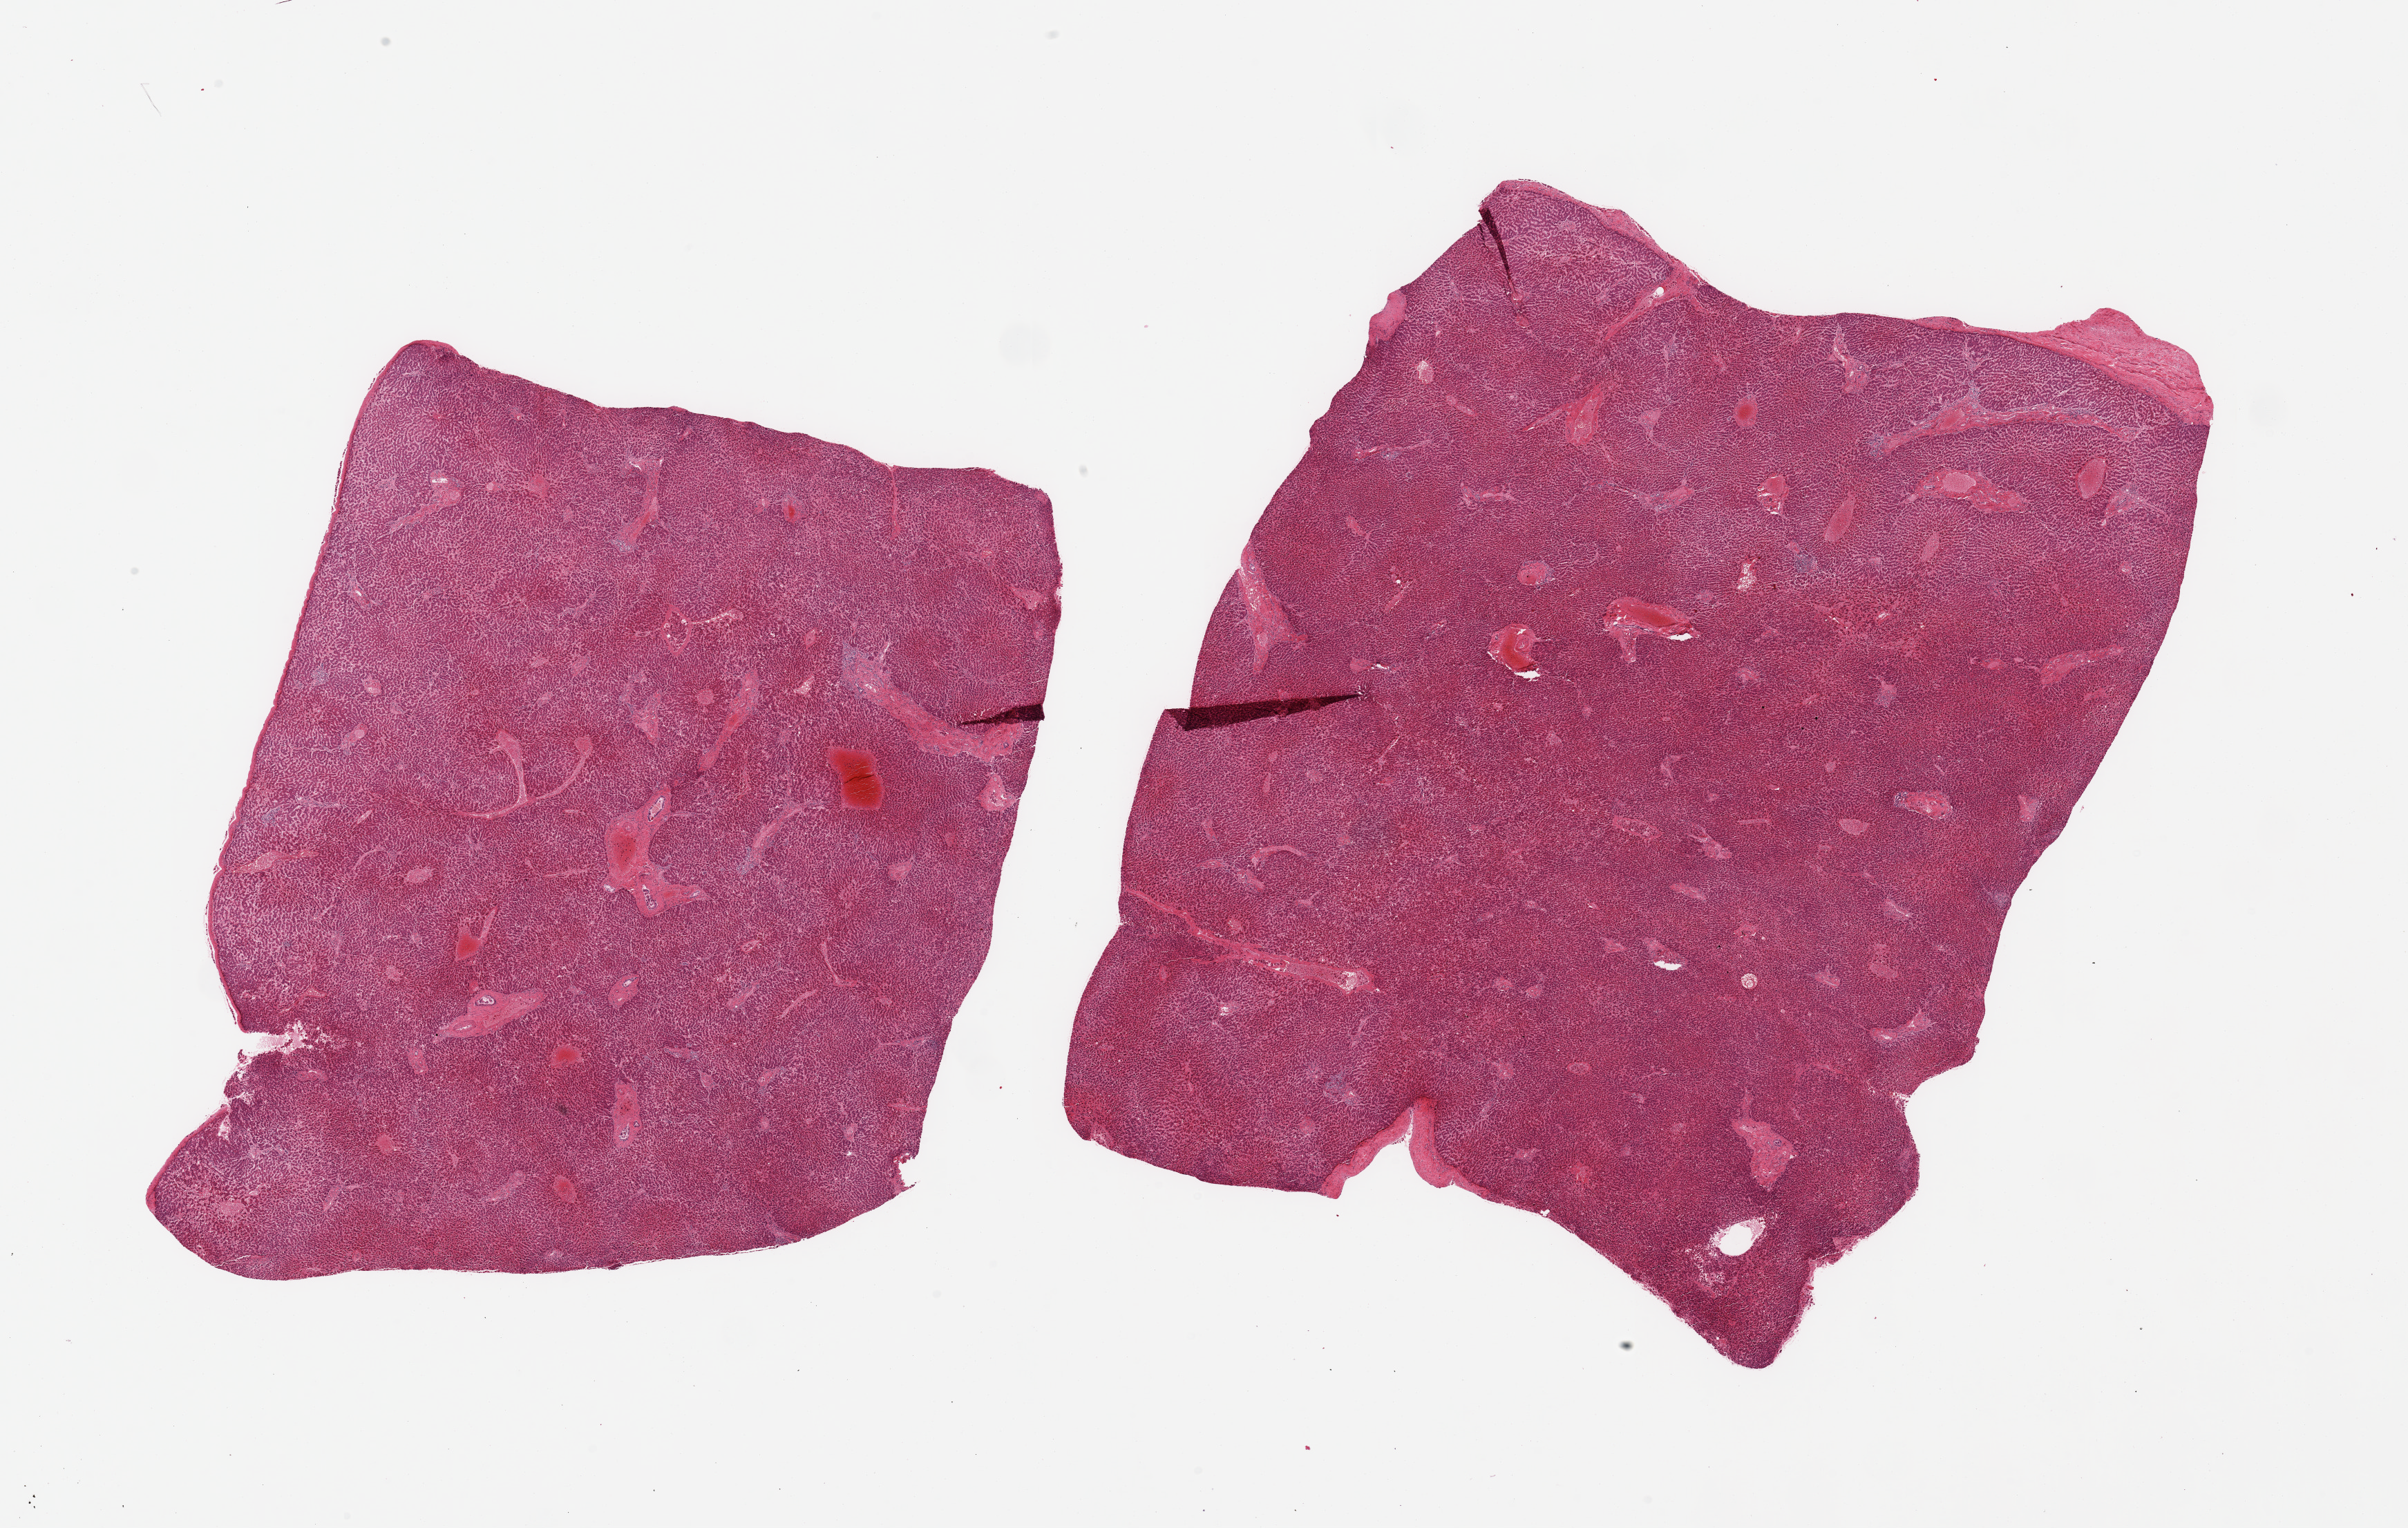
H&E whole-slide image, whole scanned area (about 27.6 x 17.5 mm, acquisition: 20x scan) shown as a low-resolution overview, PAXgene-fixed paraffin-embedded (PFPE) section, section of liver (target tissue), donor tissue sample. Donor: male.
Pathologist's review note for this sample: 2 pieces; includes portion of capsule (not target), central congestion.